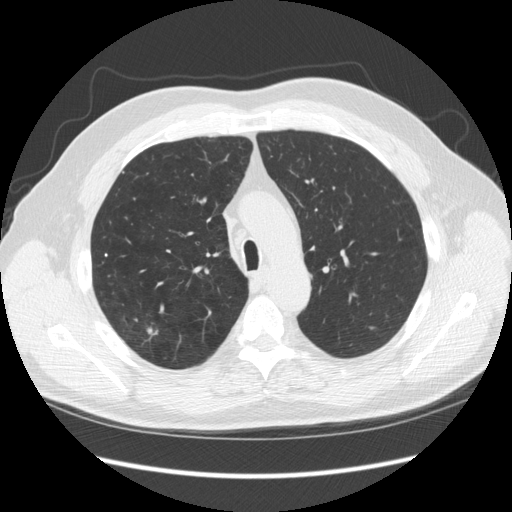
Low-dose screening chest CT, one axial slice. Position 178 of 248 along the scan axis. Reconstruction kernel STANDARD. Lung window (W 1500 / L -600 HU). 512 × 512 image matrix, field of view 380 × 380 mm.
Outlined on this slice (outlined manually by an expert reader):
- lesion 1 (tumor, upper lobe of right lung): bounding box [x1, y1, x2, y2] px = [147, 328, 153, 334]